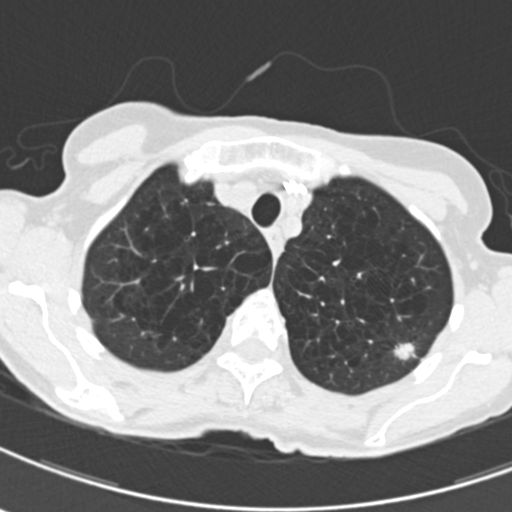
Chest CT (low-dose screening protocol), one axial image, third screening round (two years after baseline), lung window (W 1500 / L -600 HU), 2 mm slice thickness, 120 kVp. Female, age 71 years at enrolment.
Lesion marked by an expert reader, bounding box <387,330,430,370> (left, top, right, bottom; pixels). The exam's reader record, not a measurement of the box and not confirmed to be the same lesion: non-calcified nodule or mass ≥4 mm, left upper lobe, 12 × 9 mm, spiculated (stellate) margins, mixed attenuation, pre-existing on the prior screen: yes; interval growth: yes. Later outcome: lung cancer diagnosed 114 days after this screen — adenocarcinoma, NOS, left upper lobe, moderately differentiated (G2), stage IA (AJCC 6th edition), 12 mm at pathology.